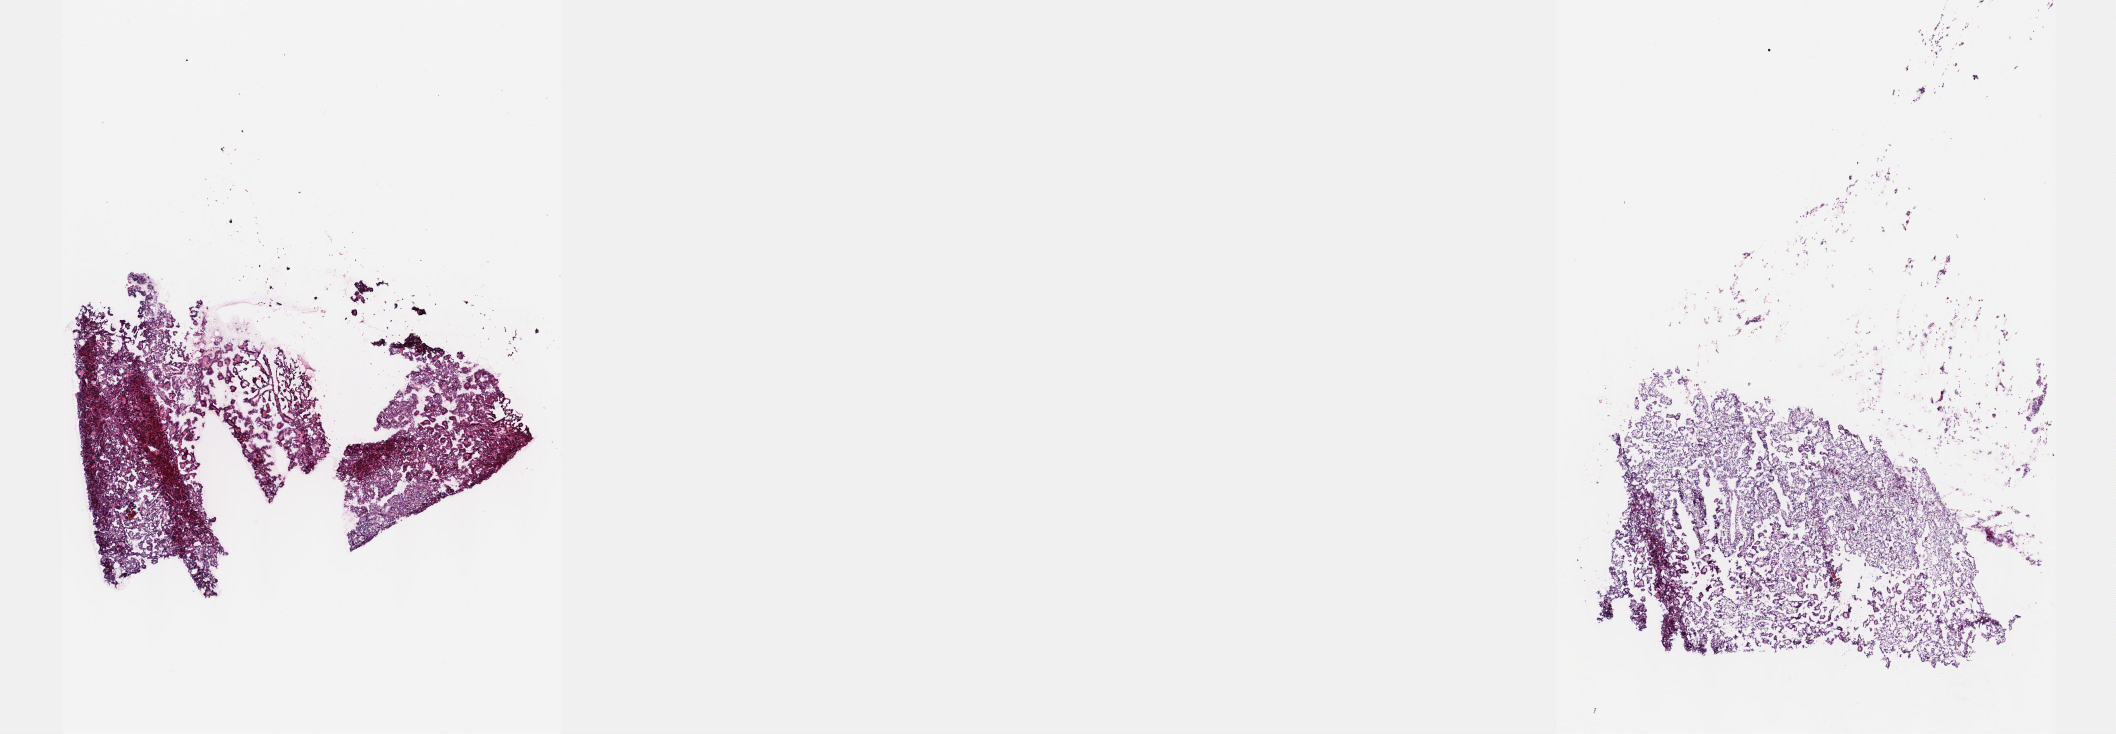
Whole-slide histology image, Hematoxylin and eosin (H&E) stained, low-resolution overview of the scanned area, about 17.1 x 5.9 mm (slide scanned at 40x), frozen section, primary tumour sample from the kidney. Male patient; age at initial diagnosis 74 years. Slide review estimates, as recorded: tumour cells 100%, tumour nuclei 80%, normal cells 0%, stromal cells 0%, necrosis 0%. Infiltration values recorded for this section: lymphocyte infiltration 1%, monocyte infiltration 1%, neutrophil infiltration 0%.
AJCC pathologic stage: I (7th edition). Laterality: left. Diagnosis: Papillary adenocarcinoma, NOS.